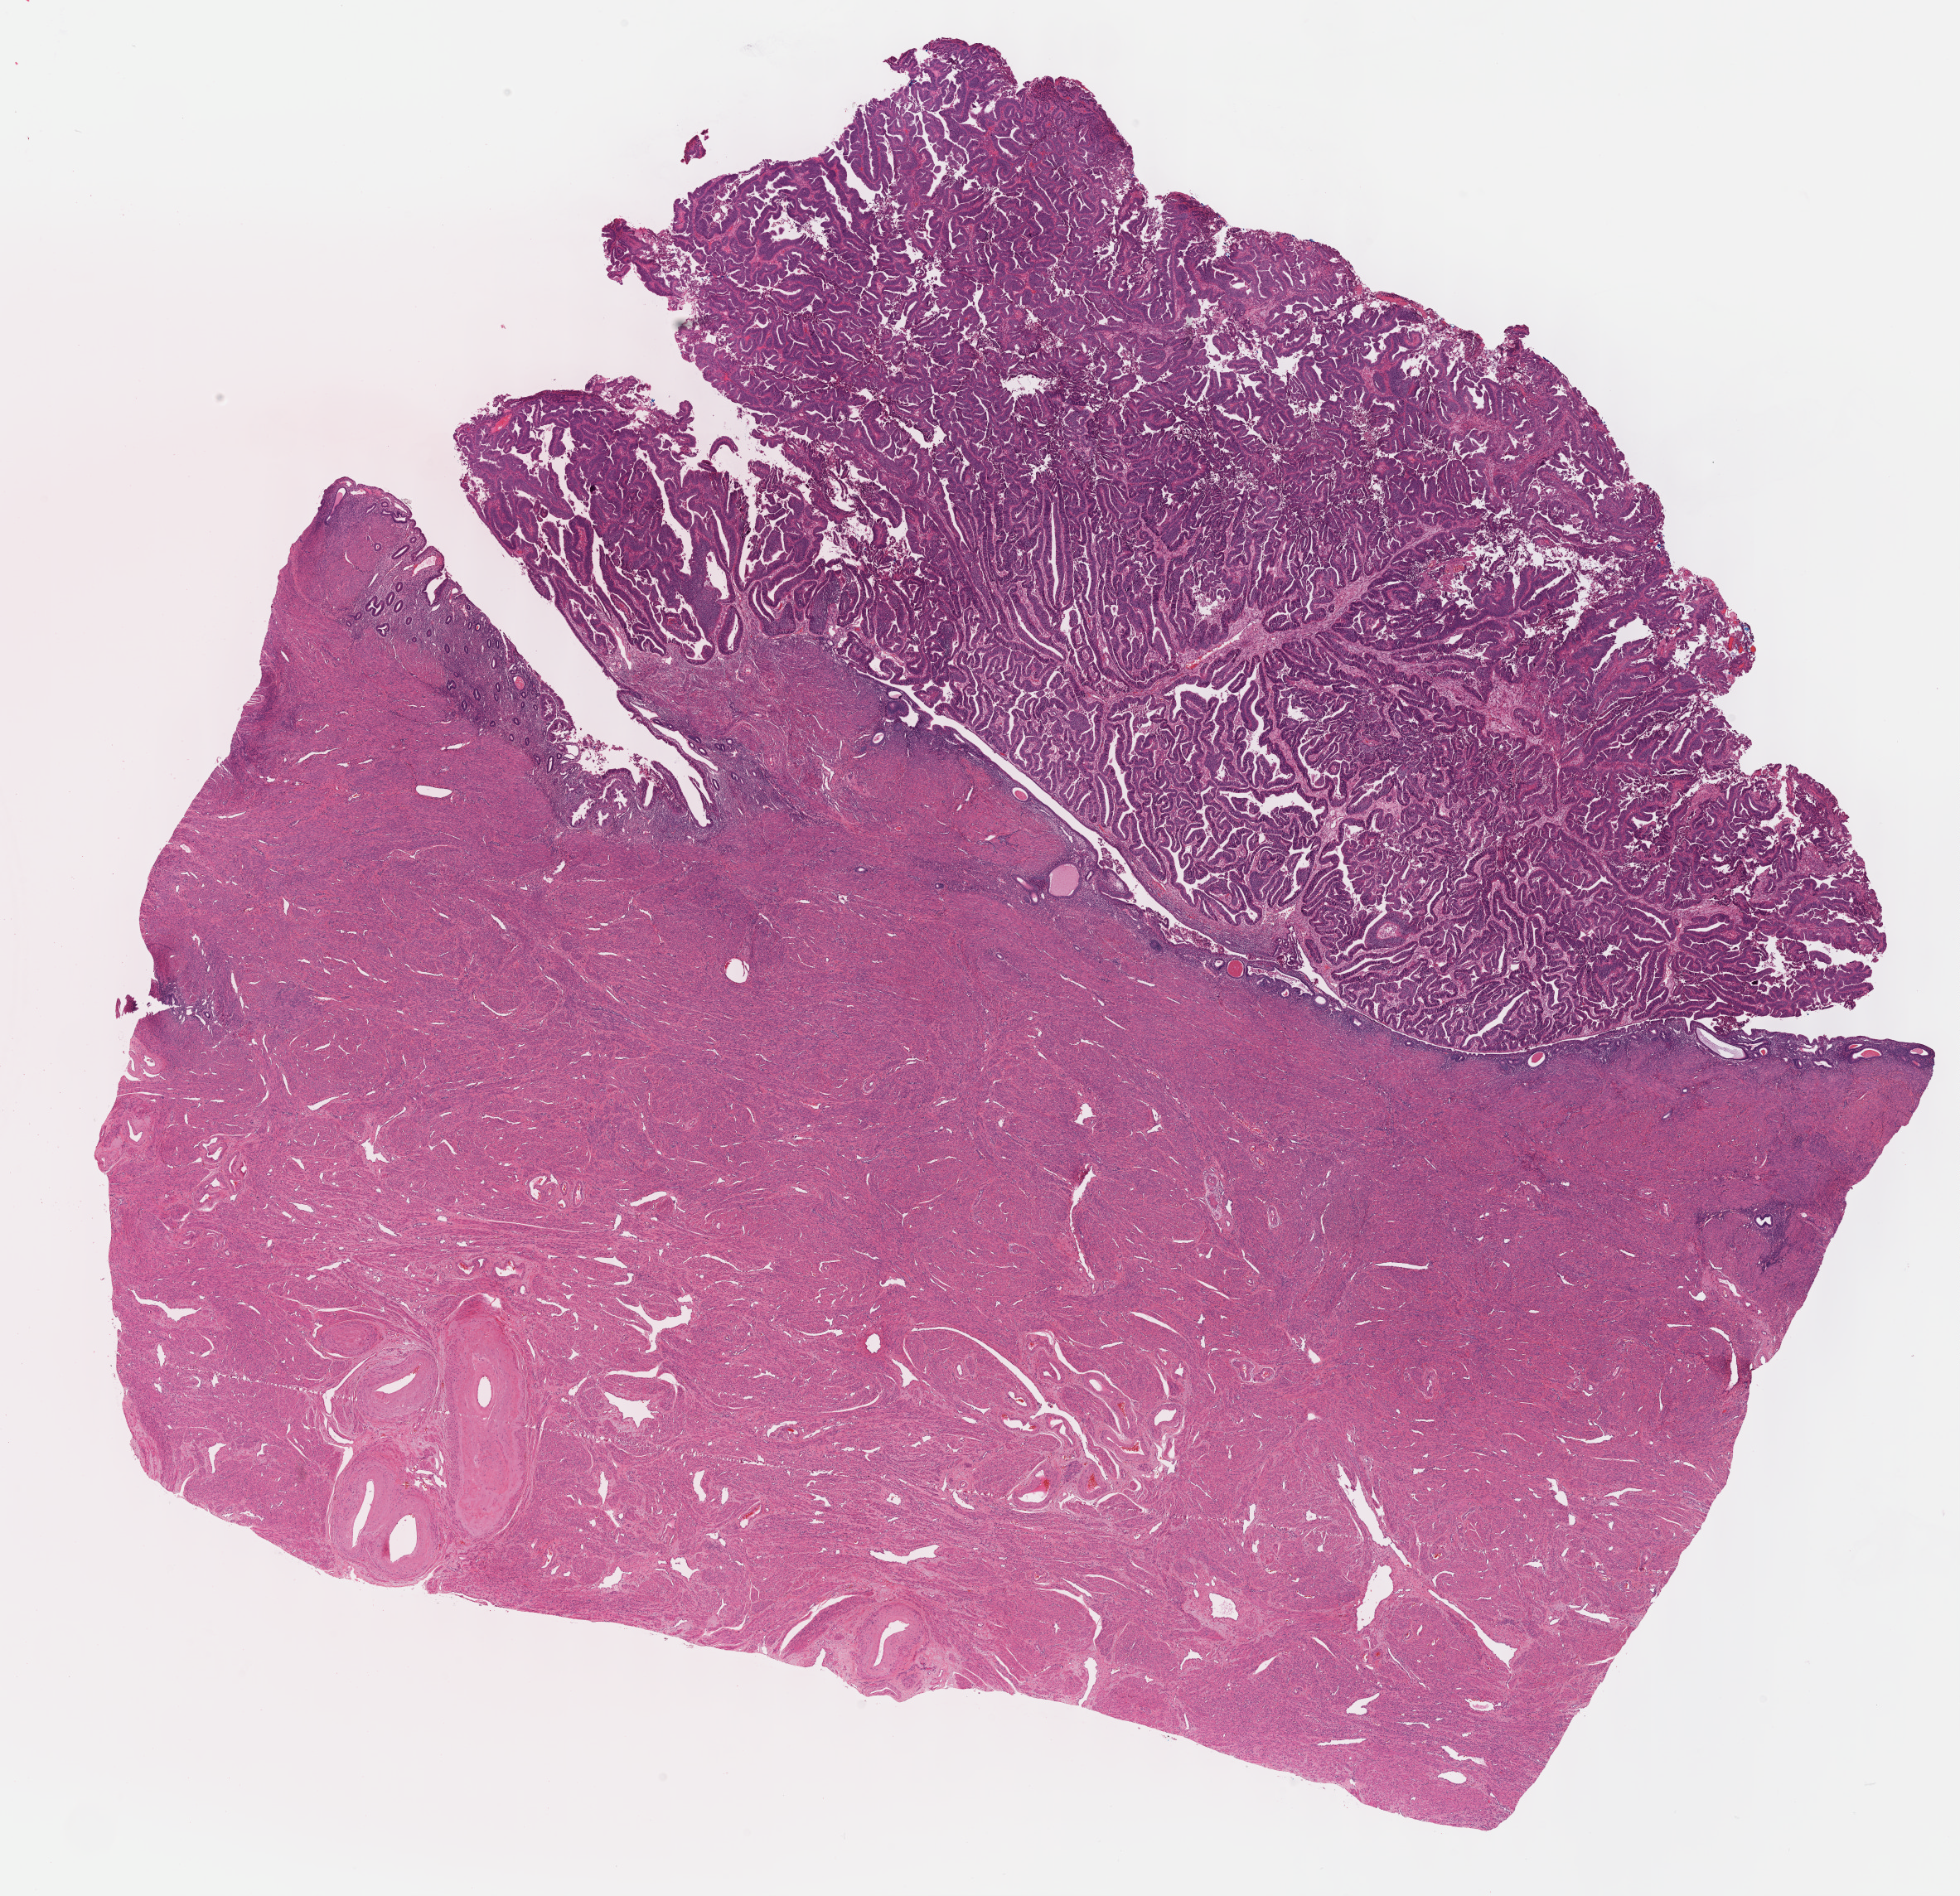
Digitized Hematoxylin and eosin (H&E) stained tissue section (whole slide), a low-resolution overview of the entire scanned area, about 19.1 x 18.5 mm (acquisition: 40x scan). FFPE section. Uterus, primary tumour sample. Patient: female, age at initial diagnosis 71 years. Histologic grade: G3 (poorly differentiated).
Histologic diagnosis: Serous cystadenocarcinoma, NOS (endometrium). FIGO stage: IA.